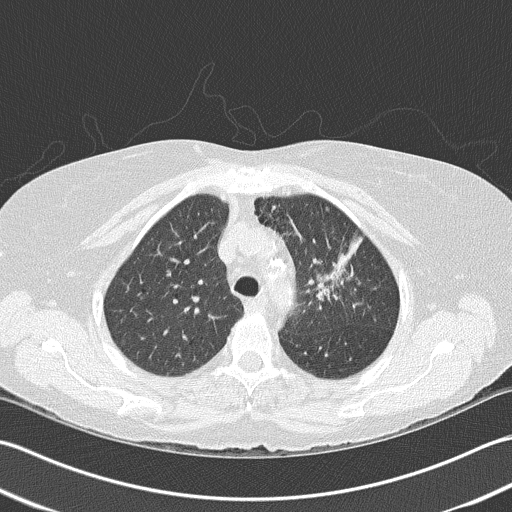
Low-dose screening chest CT, axial slice, baseline annual screen, lung window (W 1500 / L -600 HU), lung (sharp) reconstruction kernel (B50f), slice 122 of 159 in the series, 512 × 512 image matrix, field of view 350 × 350 mm. Female participant, aged 68 years at enrolment.
Expert-annotated lung lesion, box from (x=296, y=227) to (x=370, y=311) px. Screening reader's record for this exam: no non-calcified nodule ≥4 mm recorded. Official screen result: negative screen, minor abnormalities not suspicious for lung cancer. Lung cancer was diagnosed 763 days after this screen: adenocarcinoma, NOS, left upper lobe, poorly differentiated (G3), stage IB (AJCC 6th edition), 50 mm at pathology.